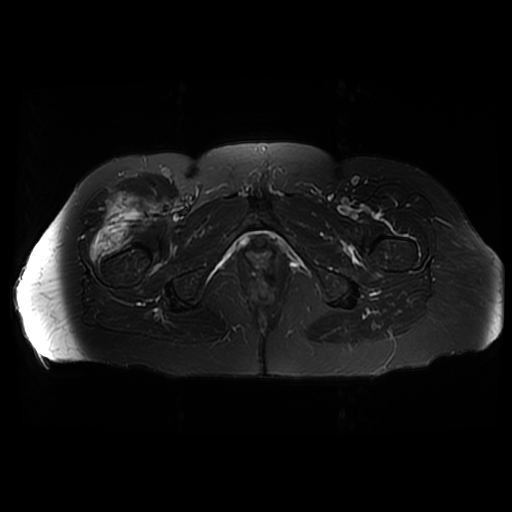
MRI of an extremity soft-tissue mass, one axial slice. Position 33 of 42 along the scan axis. T2-weighted fat-saturated. 6 mm slice thickness. 512 × 512 image matrix, field of view 440 × 440 mm. Female patient. Case-level facts recorded for this patient, not image findings: histological type: pleiomorphic undifferentiated sarcoma; grade: high; site of the primary tumour: right quadricep.
Annotated regions visible in this slice (expert manual segmentation):
- gross tumour volume including surrounding oedema: box from (x=89, y=191) to (x=155, y=261) px